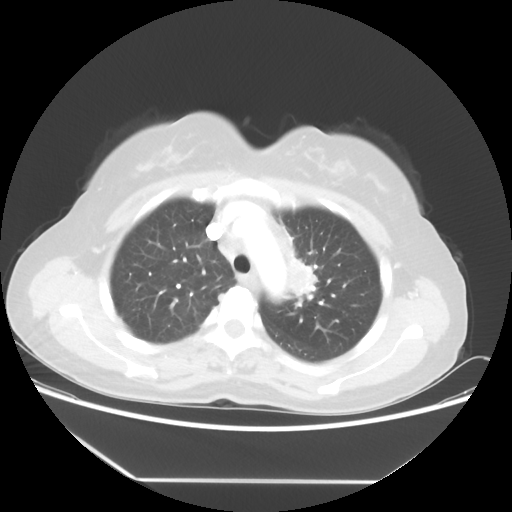
Chest CT, one axial slice. Position 40 of 52 along the scan axis. Reconstruction kernel STANDARD. Lung window (W 1500 / L -600 HU). 5 mm slice thickness. 512 × 512 image matrix, field of view 390 × 390 mm. Patient: female, 50 years. Case-level facts recorded for this patient, not image findings: clinical TNM (as recorded): T2 N3 M0.
Annotated regions visible in this slice (rectangle marked by the reading radiologist):
- lung tumour (recorded histology: adenocarcinoma): bounding box <287,248,325,312> (left, top, right, bottom; pixels)